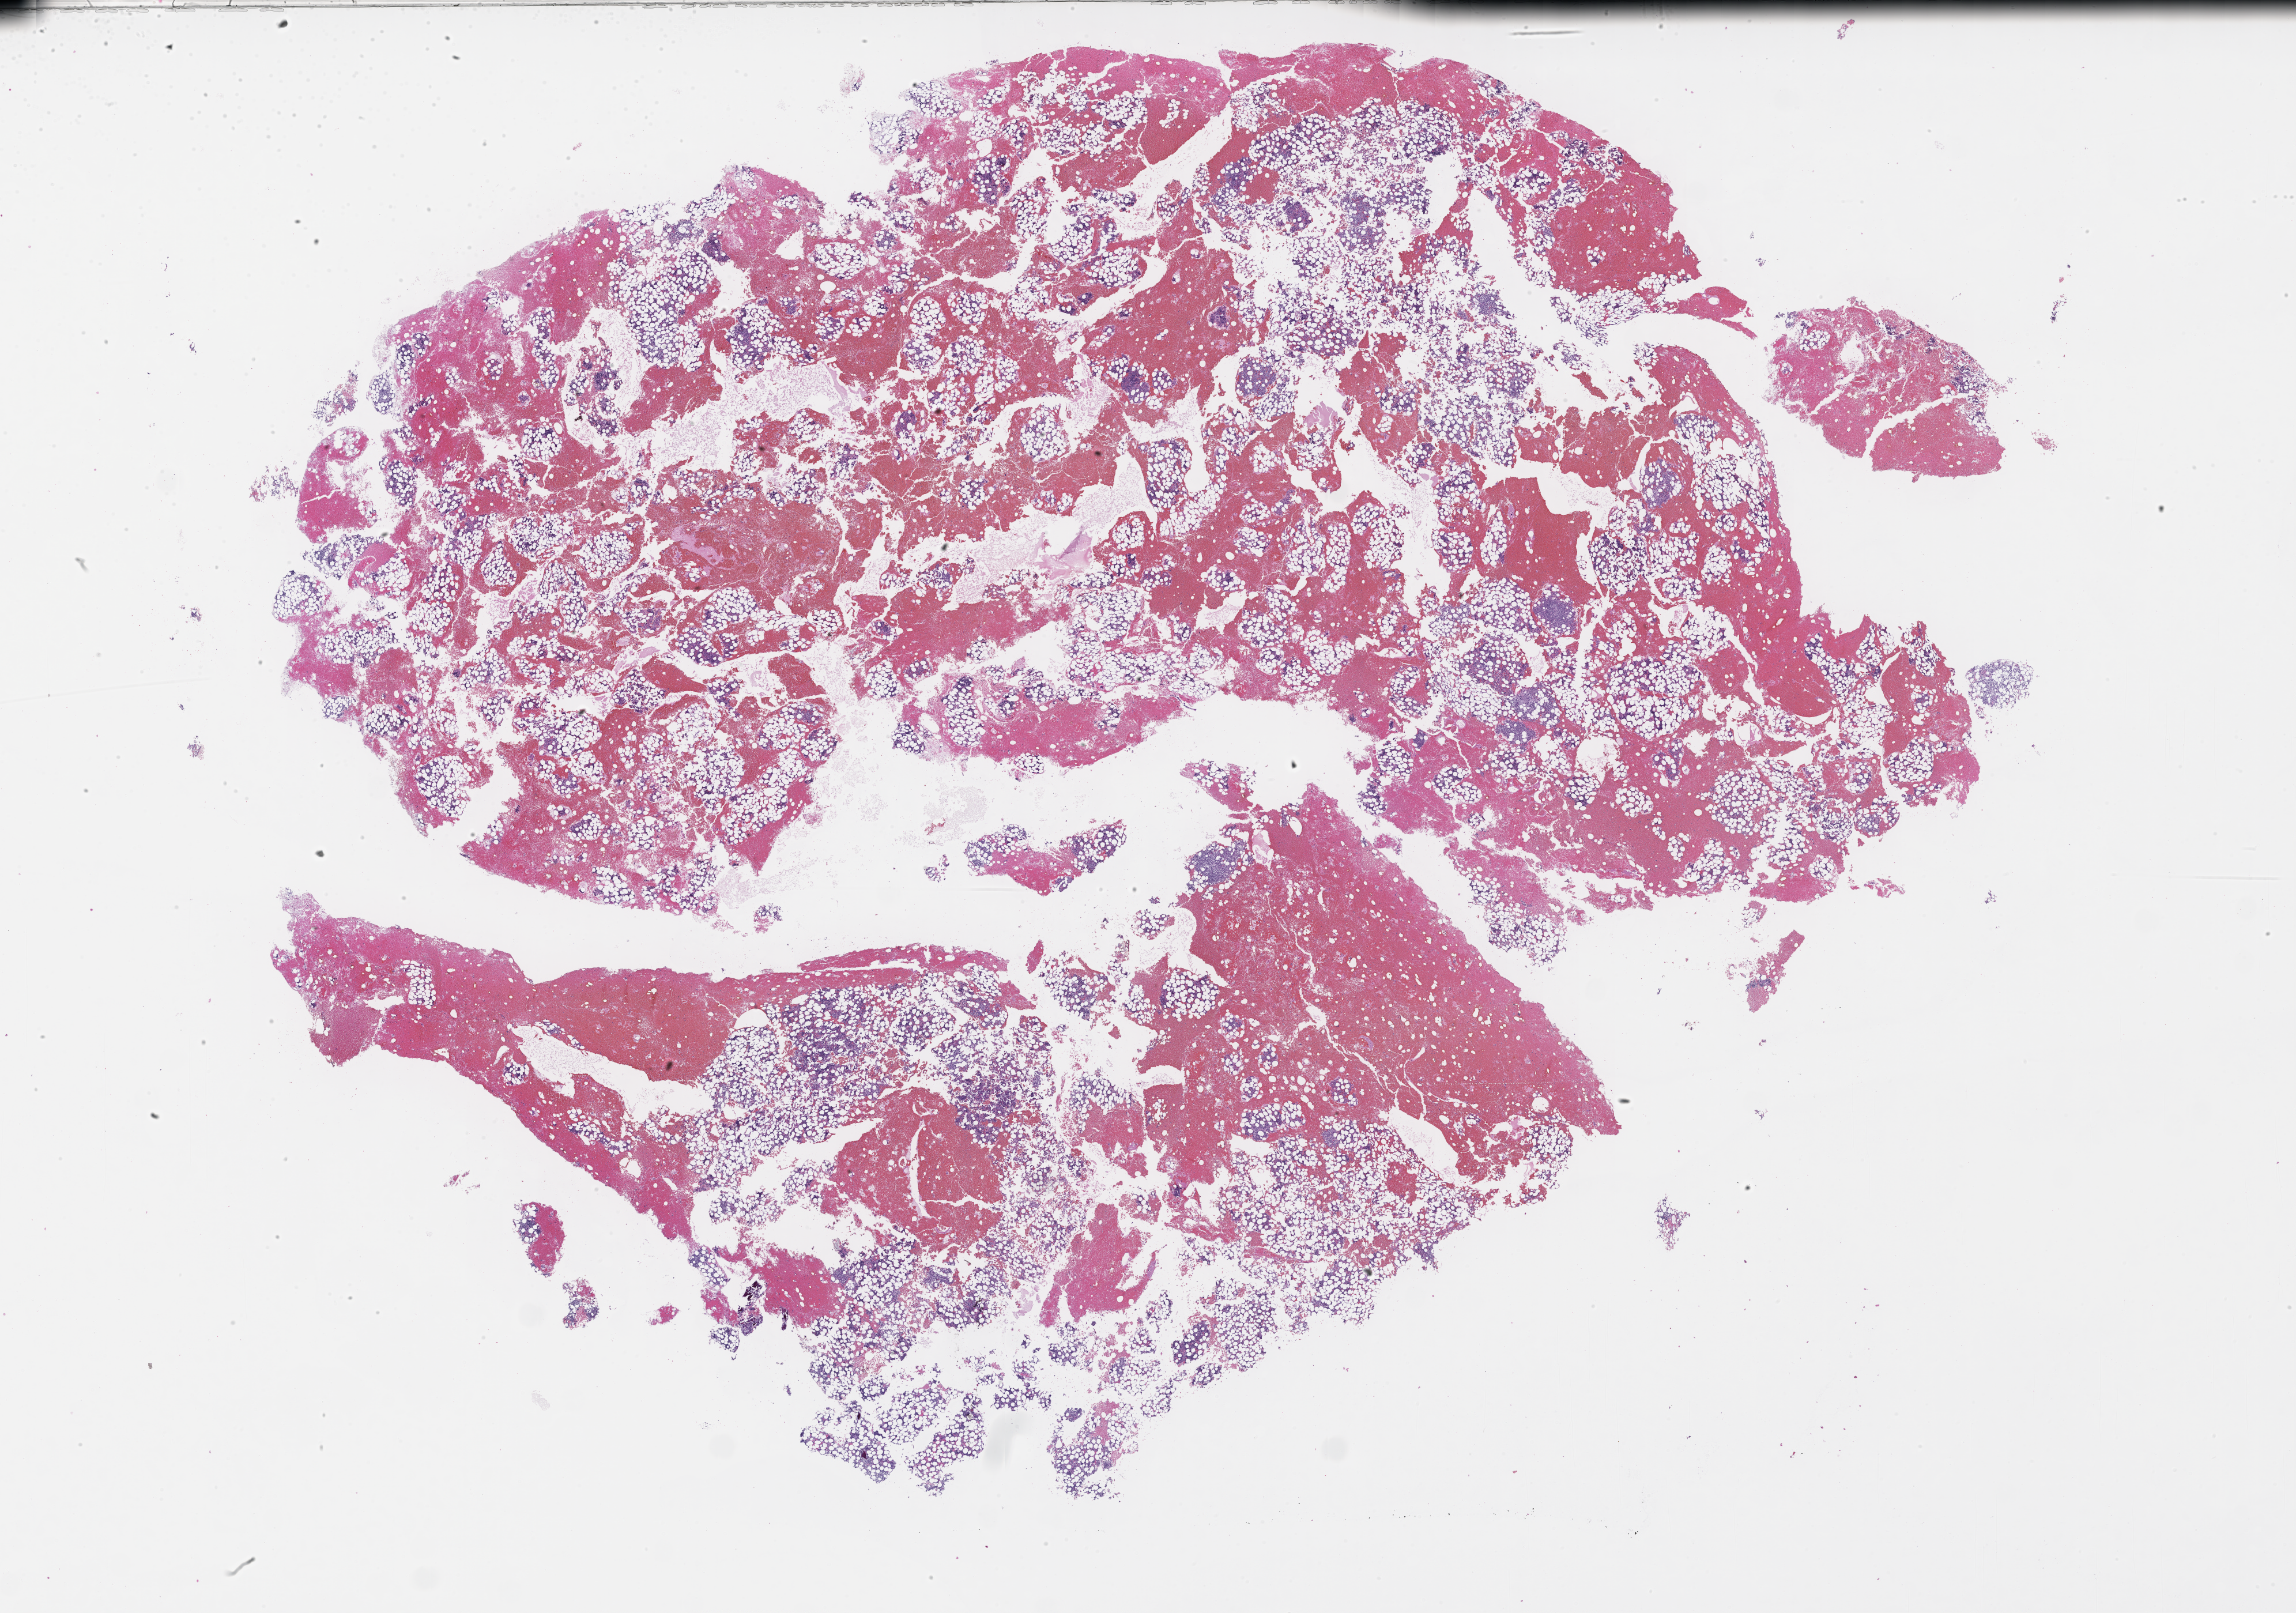
Digitized haematoxylin and eosin-stained section — shown as a low-resolution overview of the whole scanned area (about 32.2 x 22.6 mm), FFPE section, site: bone marrow, specimen time point: archival tissue. Female patient.
• patient diagnosis: Plasma Cell Myeloma